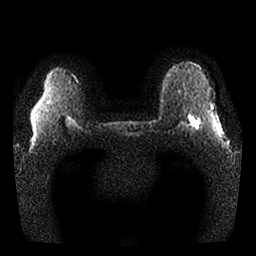
Breast MRI, one axial slice. Slice 22 of 25 in the series (ordered by position). Diffusion-weighted series; image 2 of 4 stored at this slice position (different b-values; order by instance number). 1.5 T. 4 mm slice thickness. 256 × 256 image matrix. Female patient.
Outlined on this slice (outlined manually by an expert reader):
- tumour on diffusion-weighted imaging: bounding box (x1, y1, x2, y2) in pixels: (190, 118, 199, 128)